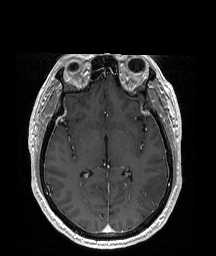
Brain MRI from a brain-tumour surgery series, one axial slice; slice 102 of 192 in the series (ordered by position); T1-weighted post-contrast; 1 mm slice thickness; 216 × 256 image matrix, field of view 219 × 260 mm. Case-level facts recorded for this patient, not image findings: histopathology: Glioblastoma; WHO grade: 4; IDH mutation: no; tumour location: Left Temporal Parietal.
Annotated regions visible in this slice (expert manual segmentation):
- tumour: bounding box (x1, y1, x2, y2) in pixels: (140, 176, 168, 206)